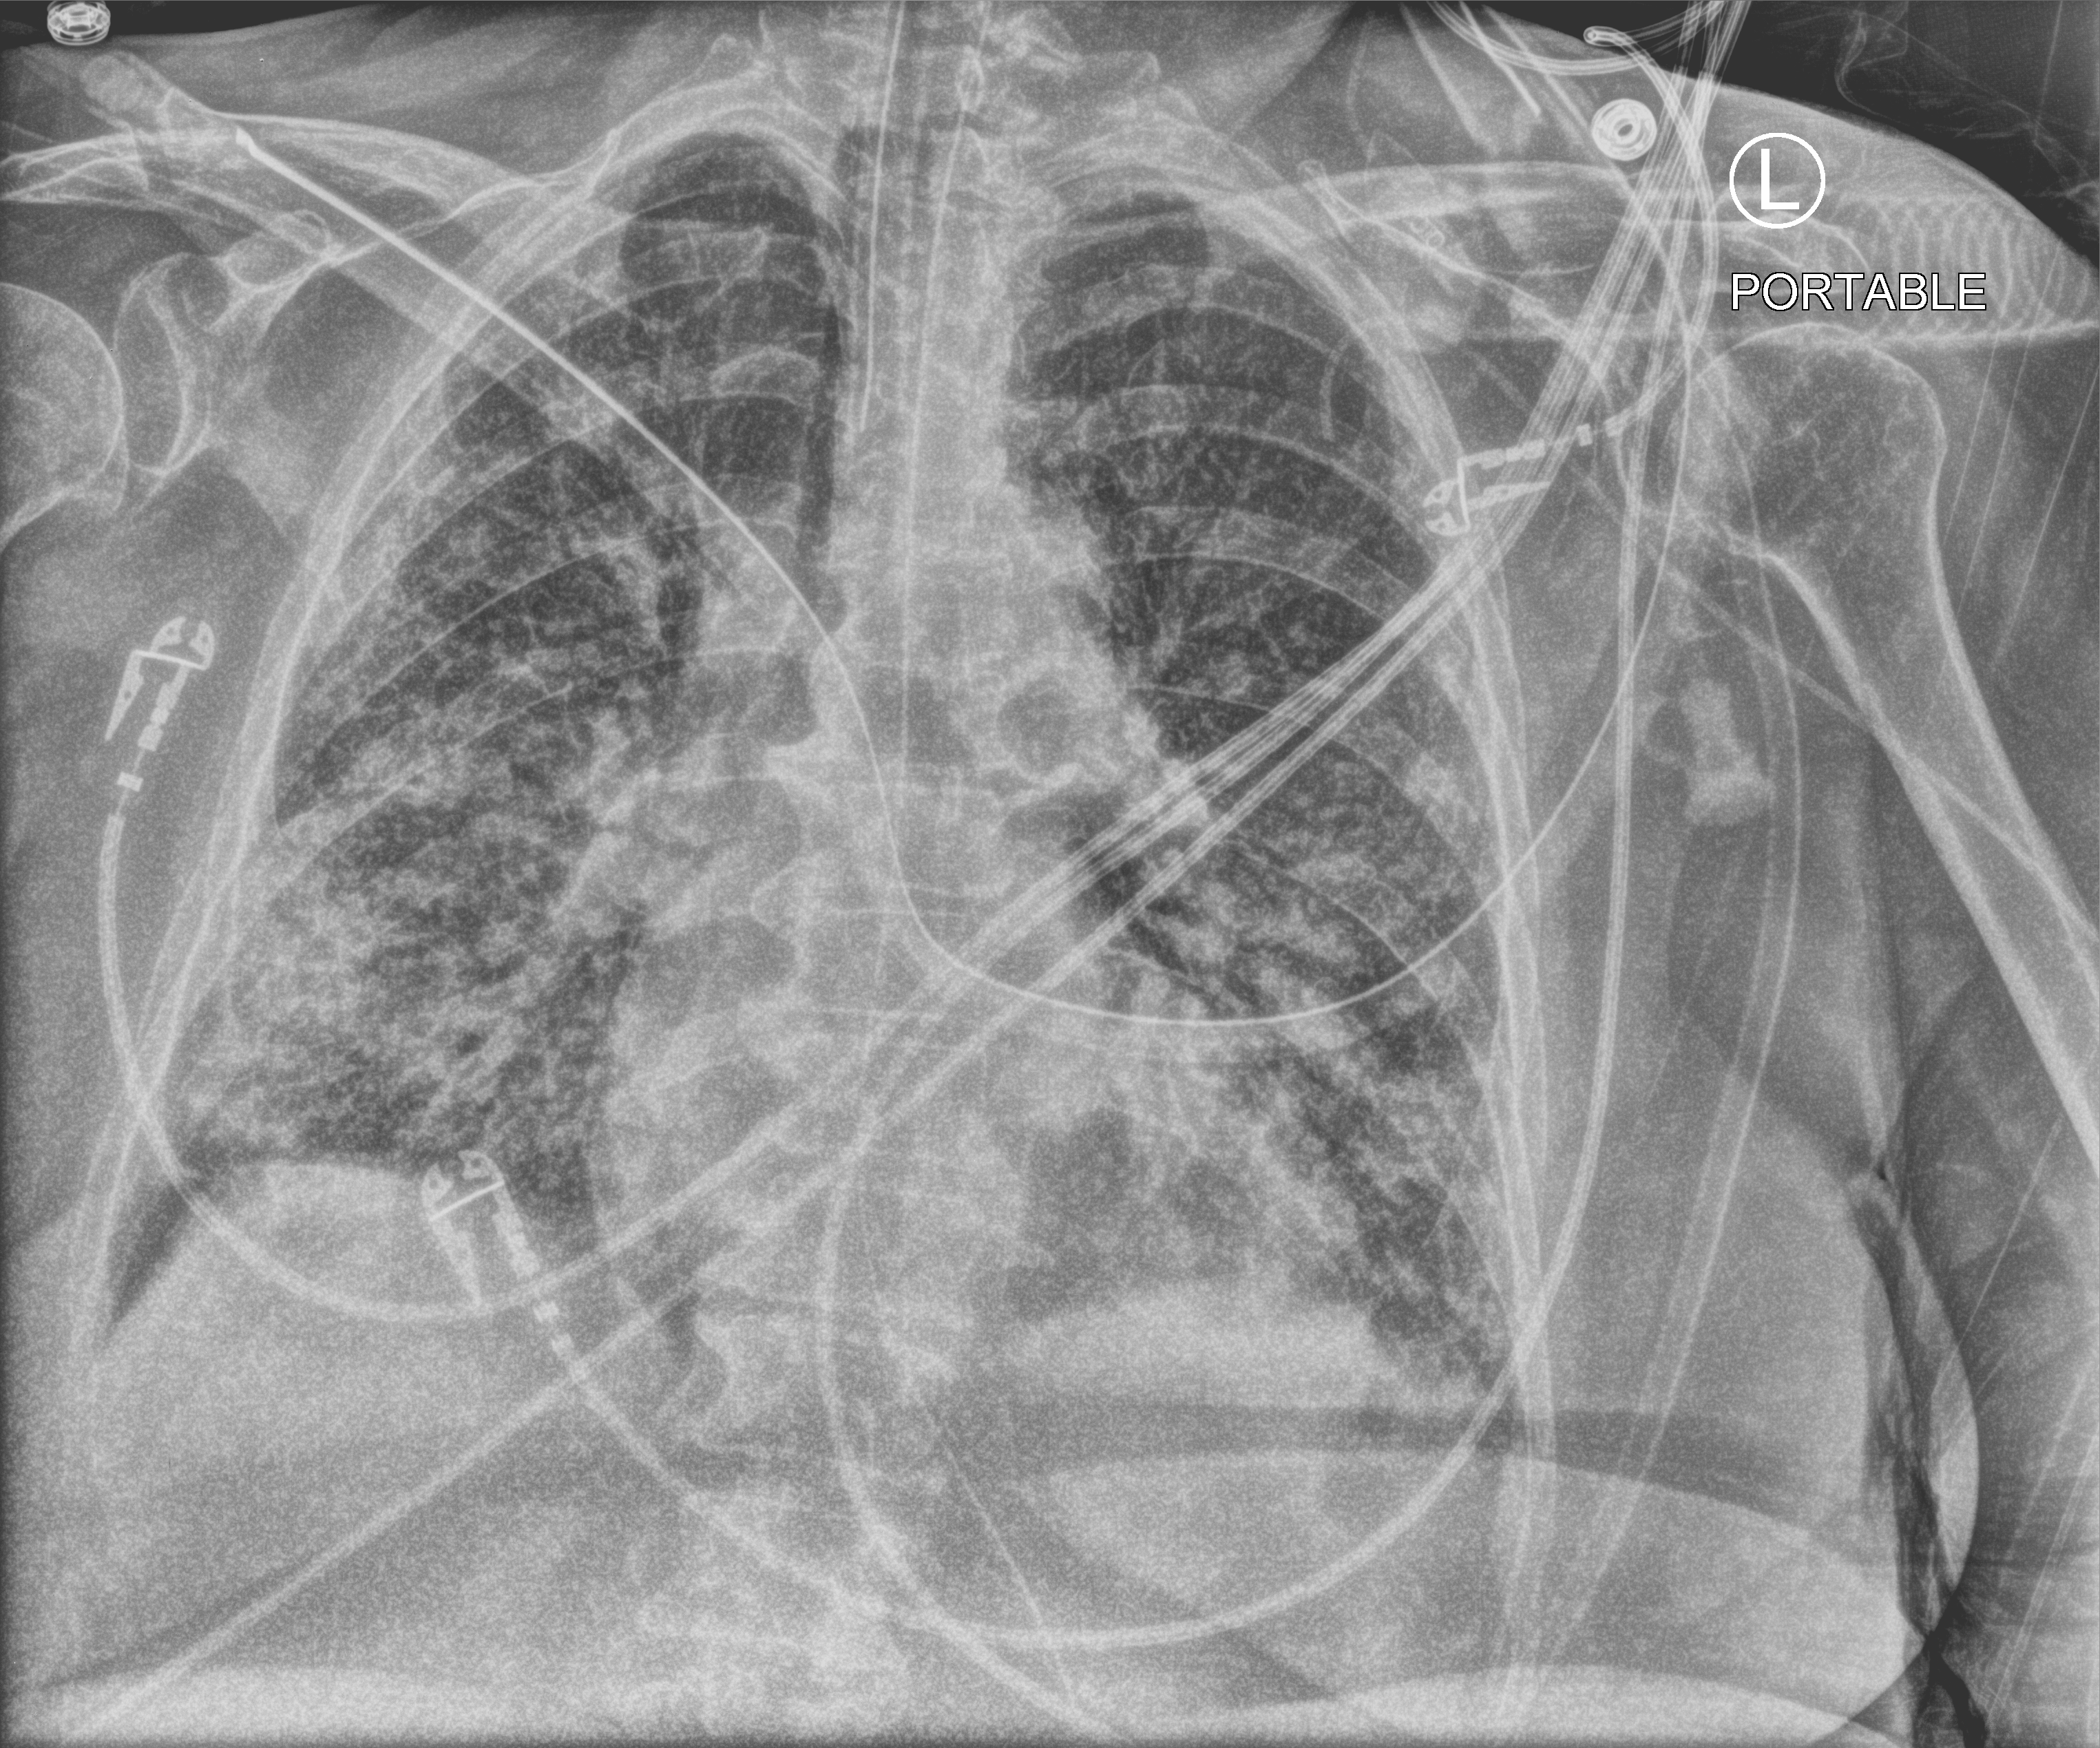
Portable chest radiograph, anteroposterior (AP) projection. Patient hospitalised with COVID-19; female, aged 75–90 years.
From the hospital-stay record, not from the radiograph (when in the stay this image was taken is not recorded): COPD (admission record): no.